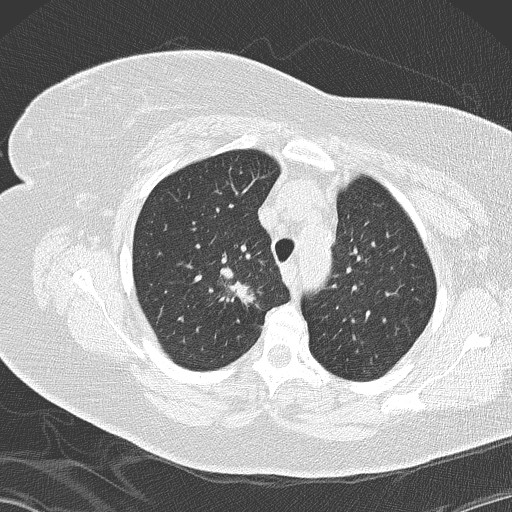
Axial slice from a low-dose chest CT screening exam. Second screening round (one year after baseline). Lung window (W 1500 / L -600 HU). 2 mm slice thickness. Lung (sharp) reconstruction kernel (B50f). Slice 34 of 146 in the series. 512 × 512 image matrix. Female, age 72 years at enrolment. Former smoker at enrolment.
Expert-annotated lung lesion, bounding box <179,240,264,328> (left, top, right, bottom; pixels). The screening reader recorded 4 non-calcified nodules or masses ≥4 mm on this exam (right lower lobe, right lower lobe, right lower lobe, right upper lobe); which of them this box marks is not recorded. Participant outcome: lung cancer diagnosed 52 days after this screen — bronchiolo-alveolar adenocarcinoma, NOS, right upper lobe, stage IIIB (AJCC 6th edition), 45 mm at pathology.